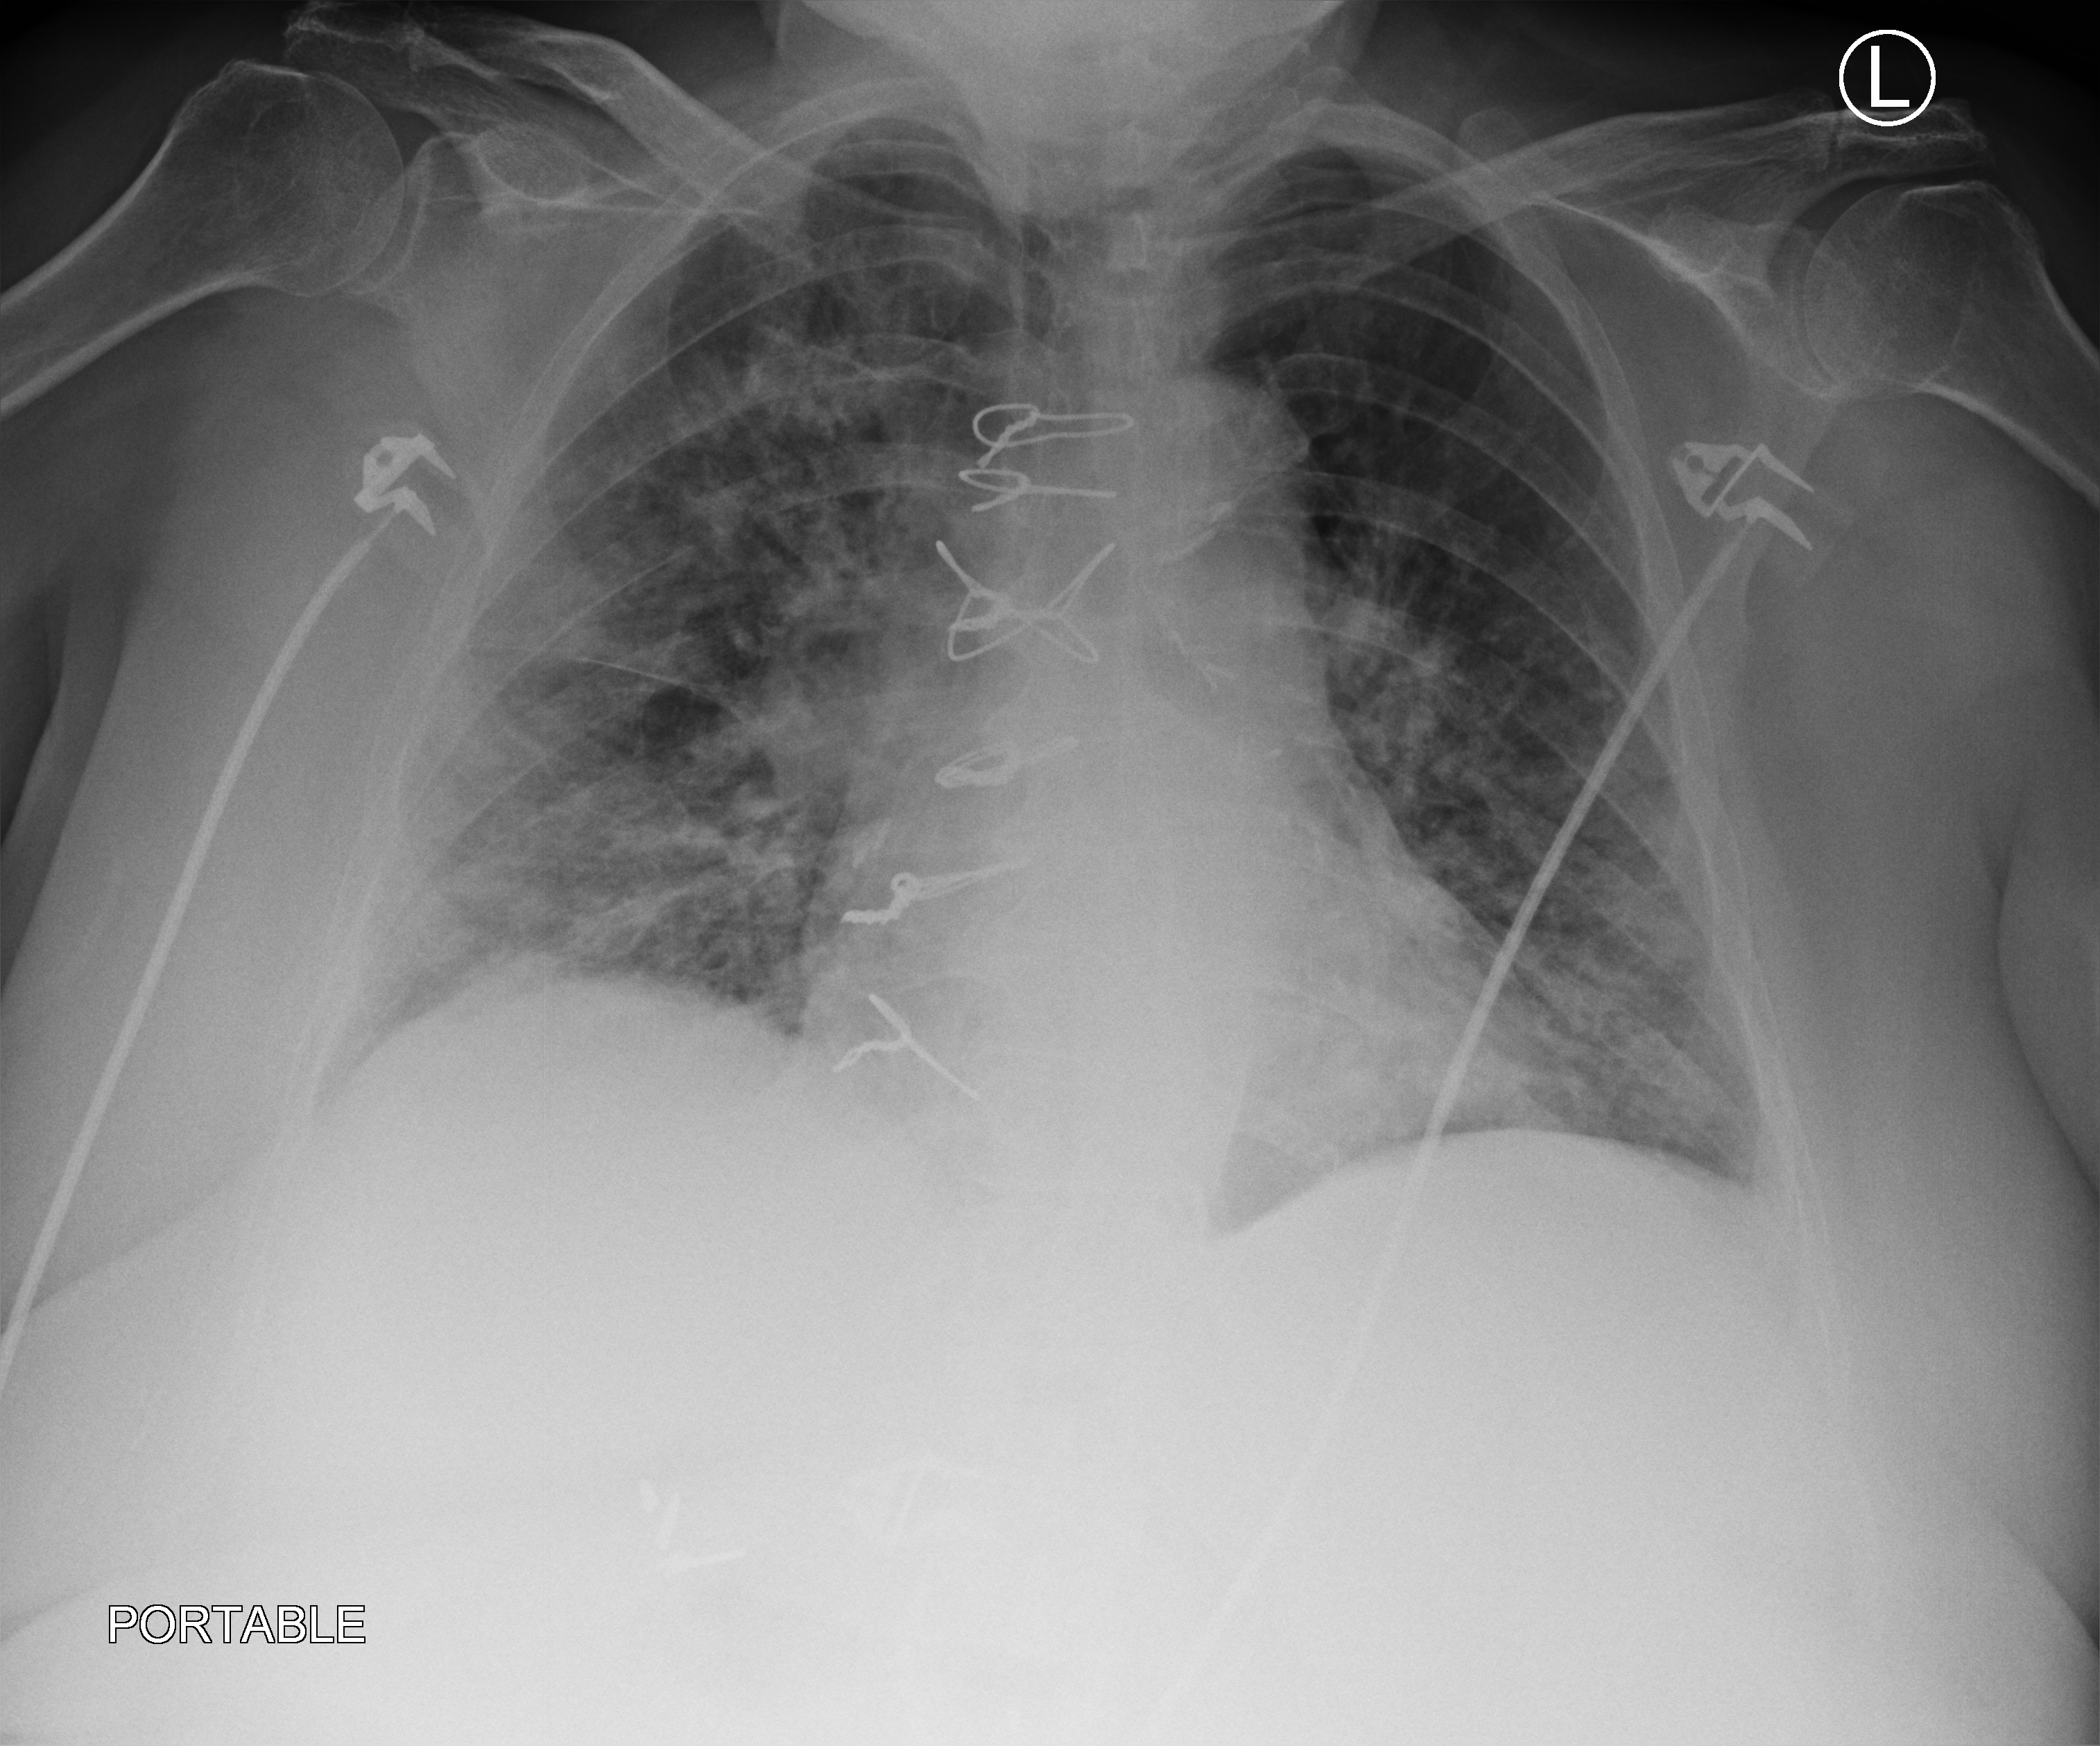
Bedside chest radiograph (computed radiography); anteroposterior (AP) projection. Patient hospitalised with COVID-19; female, aged 60–74 years.
Hospital-stay facts (about this admission, not read from this image; timing relative to this image not recorded):
- other chronic lung disease (admission record): no
- admitted to intensive care during this hospital stay: no